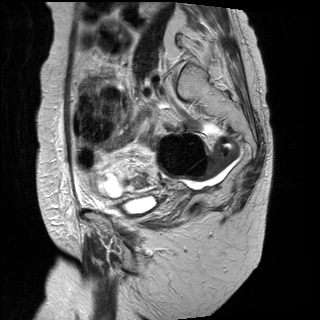
Pelvic MRI for cervical cancer, one sagittal slice. Slice 22 of 31 in the series (ordered by position). T2-weighted. 1.5 T. TE 89 ms, TR 3890 ms. 320 × 320 image matrix, field of view 260 × 260 mm. Patient: female, 61 years.
Structures marked on this image (outlined manually by an expert reader):
- uterus and cervix: bounding box [x1, y1, x2, y2] px = [131, 171, 152, 189]